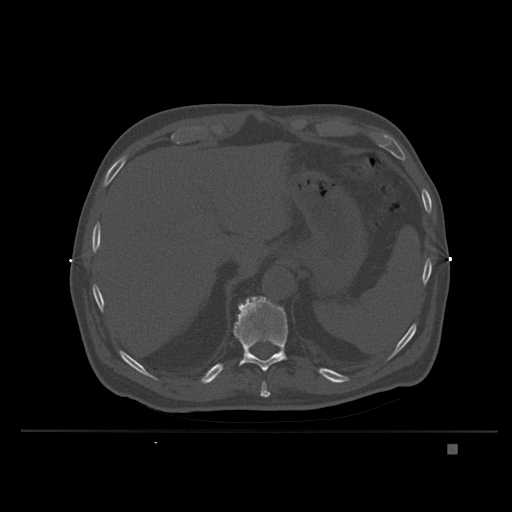
CT including the spine, one axial slice; position 177 of 435 along the scan axis; bone window (W 1800 / L 400 HU); 1.5 mm slice thickness; 512 × 512 image matrix, field of view 434 × 434 mm. Patient: male, 73 years. Case-level facts recorded for this patient, not image findings: primary cancer: skin.
Outlined on this slice (semi-automatically segmented with operator editing):
- T10 vertebra: box from (x=260, y=381) to (x=271, y=398) px
- T11 vertebra: (x=233, y=296)–(x=288, y=371)